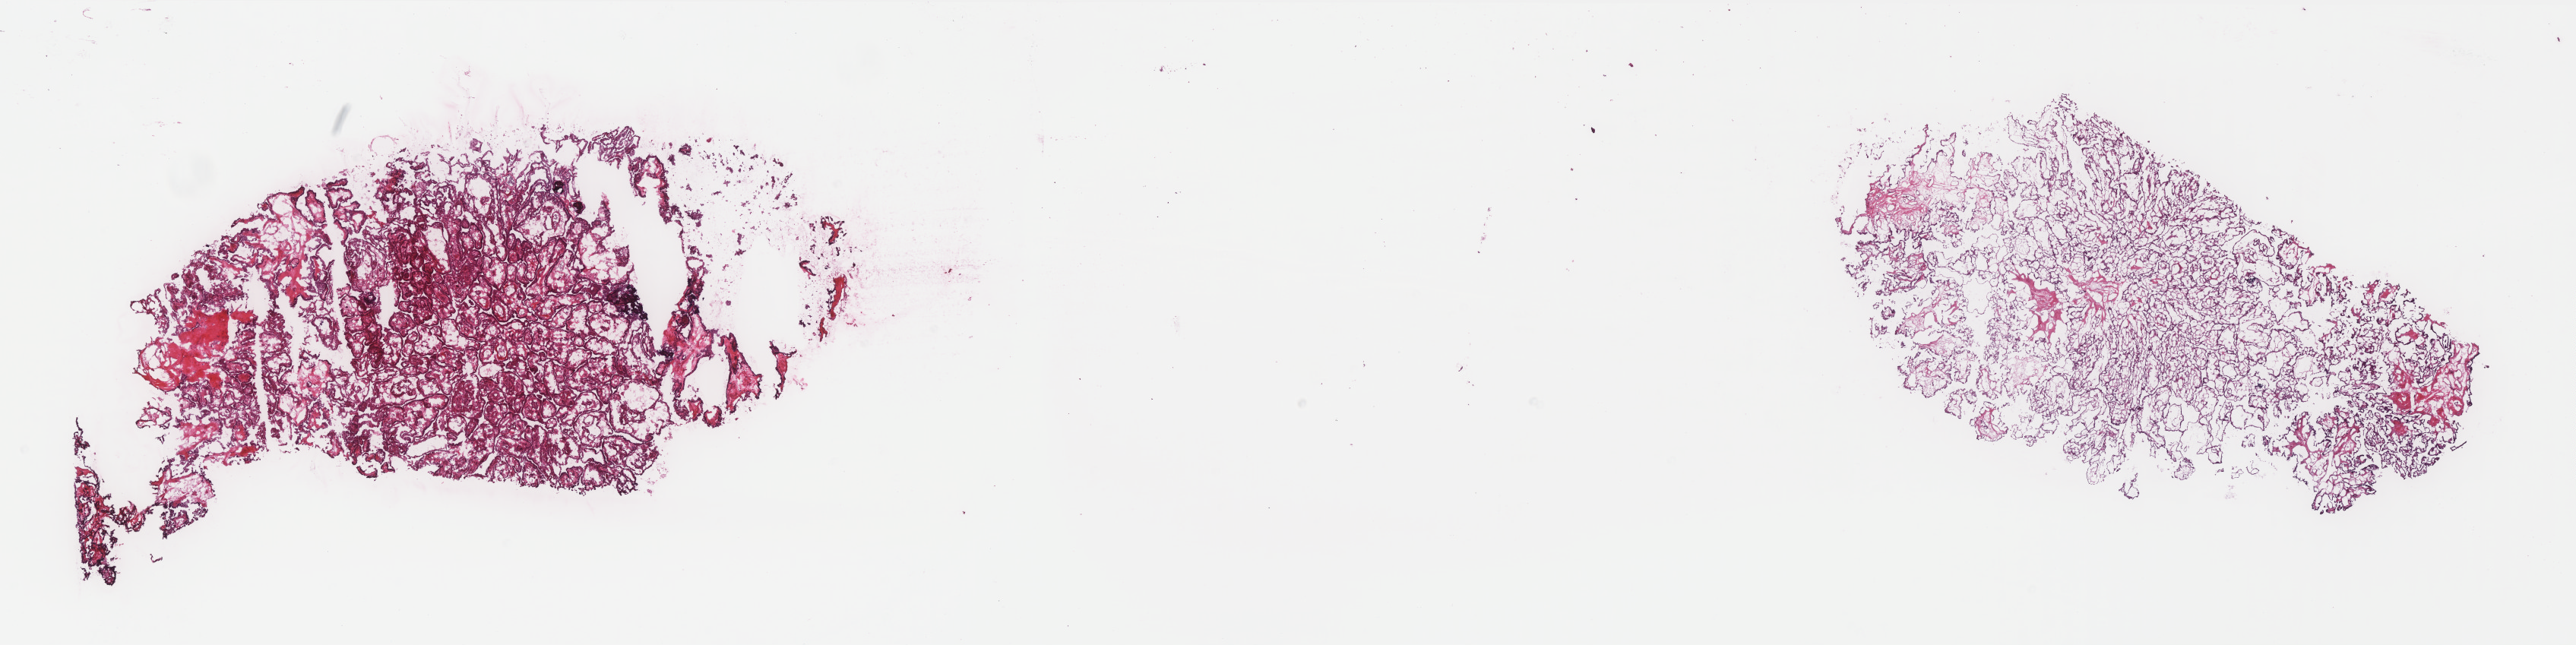
Whole-slide histology image, H&E — whole scanned area (about 27.2 x 6.8 mm, from a 40x scan) shown as a low-resolution overview. Frozen section from the top of the tissue portion. Sample: primary tumour, thyroid. Male patient; age at initial diagnosis 31 years. Slide review estimates, as recorded: tumour cells 100%, tumour nuclei 90%, normal cells 0%, stromal cells 0%, necrosis 0%. Inflammatory infiltration, as recorded: lymphocyte infiltration 0%, monocyte infiltration 0%, neutrophil infiltration 0%.
* AJCC pathologic stage: I
* laterality: left
* pathologic diagnosis: Papillary adenocarcinoma, NOS (thyroid gland)